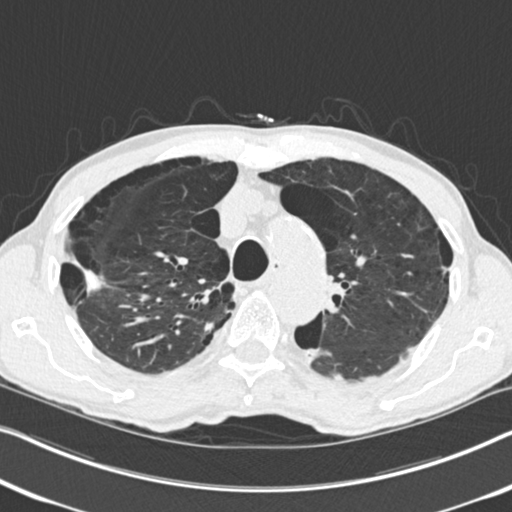
Chest CT (low-dose screening protocol), one axial image; second screening round (one year after baseline); lung window (W 1500 / L -600 HU); 2 mm slice thickness; standard (soft-tissue) reconstruction kernel (B30f); slice 68 of 251 in the series. Male participant, aged 71 years at enrolment.
Expert-annotated lung lesion, box from (x=56, y=239) to (x=127, y=316) px. The screening reader recorded 4 non-calcified nodules or masses ≥4 mm on this exam (right upper lobe, right upper lobe, right upper lobe, left upper lobe); which of them this box marks is not recorded. Later outcome: lung cancer diagnosed 83 days after this screen — adenocarcinoma, NOS, right upper lobe, well differentiated (G1), stage IA (AJCC 6th edition), 30 mm at pathology.